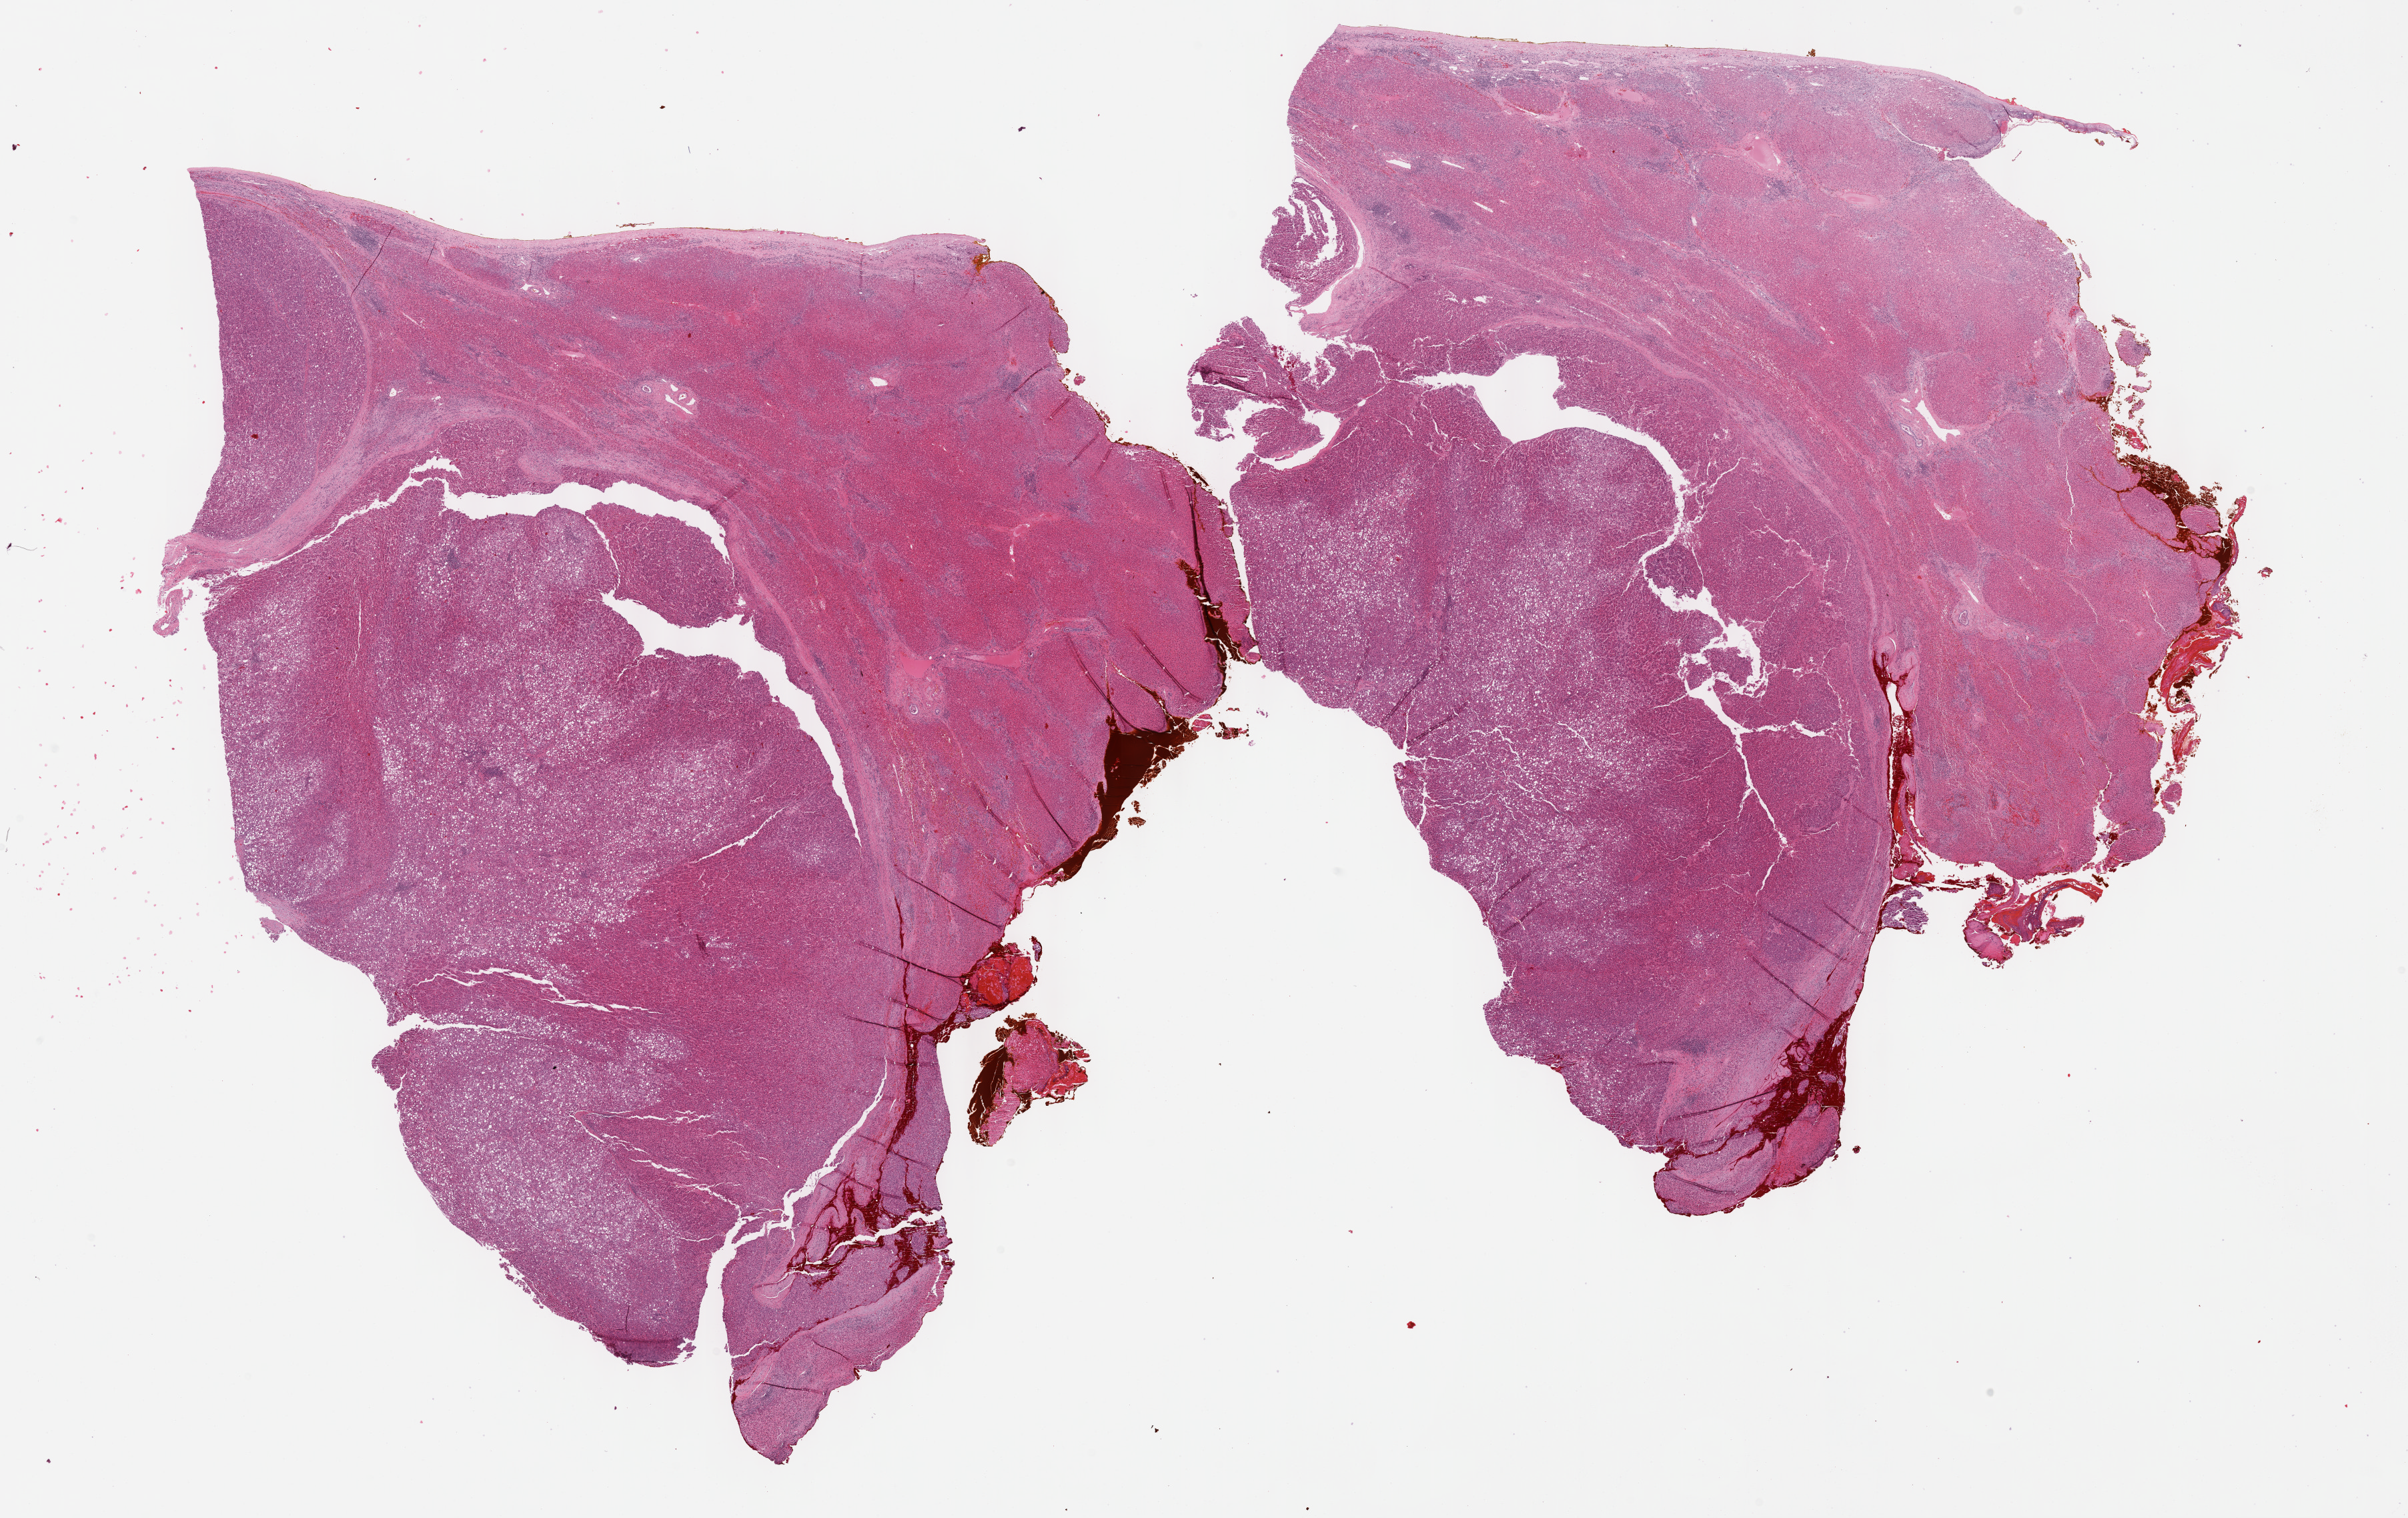
Hematoxylin and eosin (H&E) stained whole-slide image, shown as a low-resolution overview of the whole scanned area (about 29.2 x 18.4 mm); formalin-fixed paraffin-embedded (FFPE) diagnostic section; liver, primary tumour sample. Male, age 54 years at initial diagnosis. Histologic grade: G2 (moderately differentiated).
* pathologic diagnosis: Hepatocellular carcinoma, NOS
* AJCC pathologic stage: I